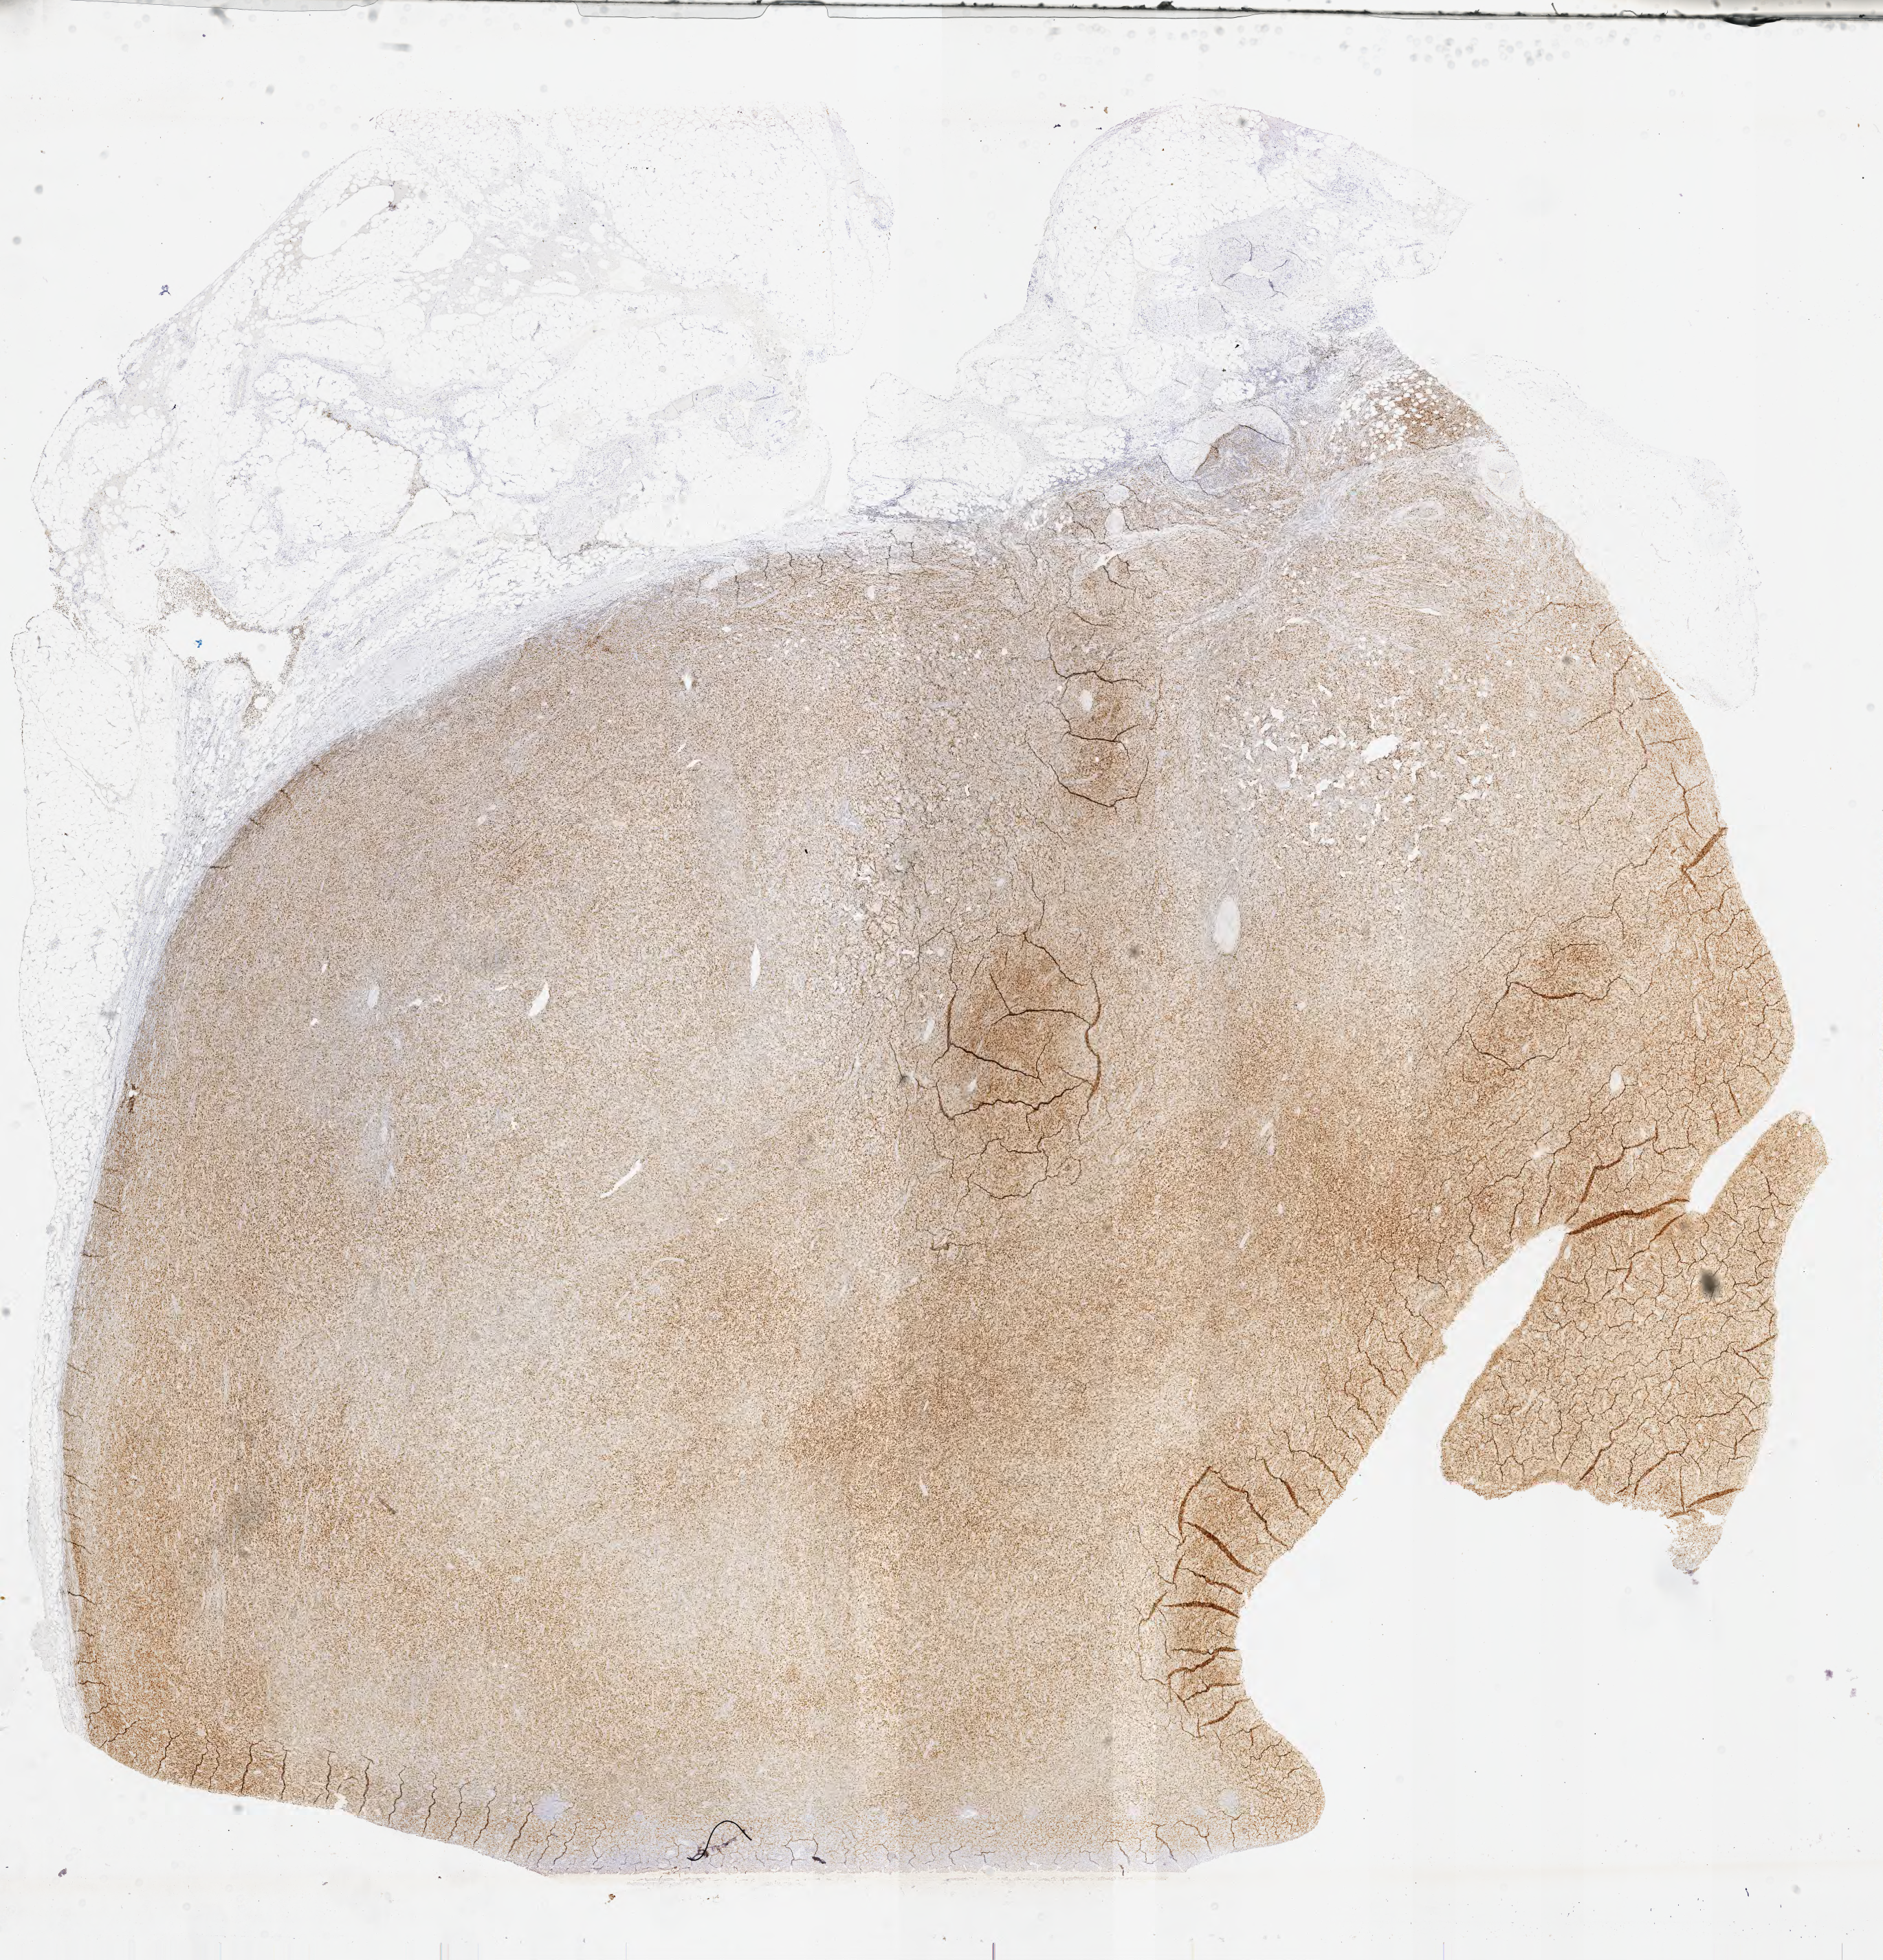
Immunohistochemistry (IHC) whole-slide image stained for IRF4/MUM1, low-resolution overview of the scanned area, about 22.1 x 23.0 mm; tumor tissue; site: lymph node. Patient: male, aged 54.
* histologic diagnosis: Diffuse large B-cell lymphoma, NOS